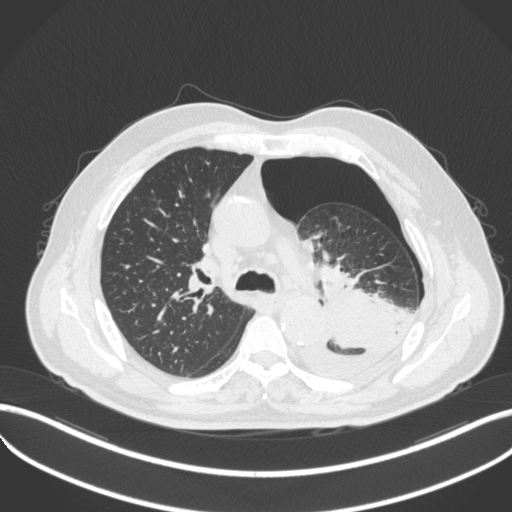
Chest CT, one axial slice. Position 339 of 466 along the scan axis. 120 kVp. Lung window (W 1500 / L -600 HU). 1 mm slice thickness. 512 × 512 image matrix, field of view 400 × 400 mm. Patient: male, 76 years. Case-level facts recorded for this patient, not image findings: clinical TNM (as recorded): T3 N0 M1b.
Outlined on this slice (bounding box drawn by a radiologist):
- lung tumour (recorded histology: adenocarcinoma): bounding box (x1, y1, x2, y2) in pixels: (292, 293, 398, 382)